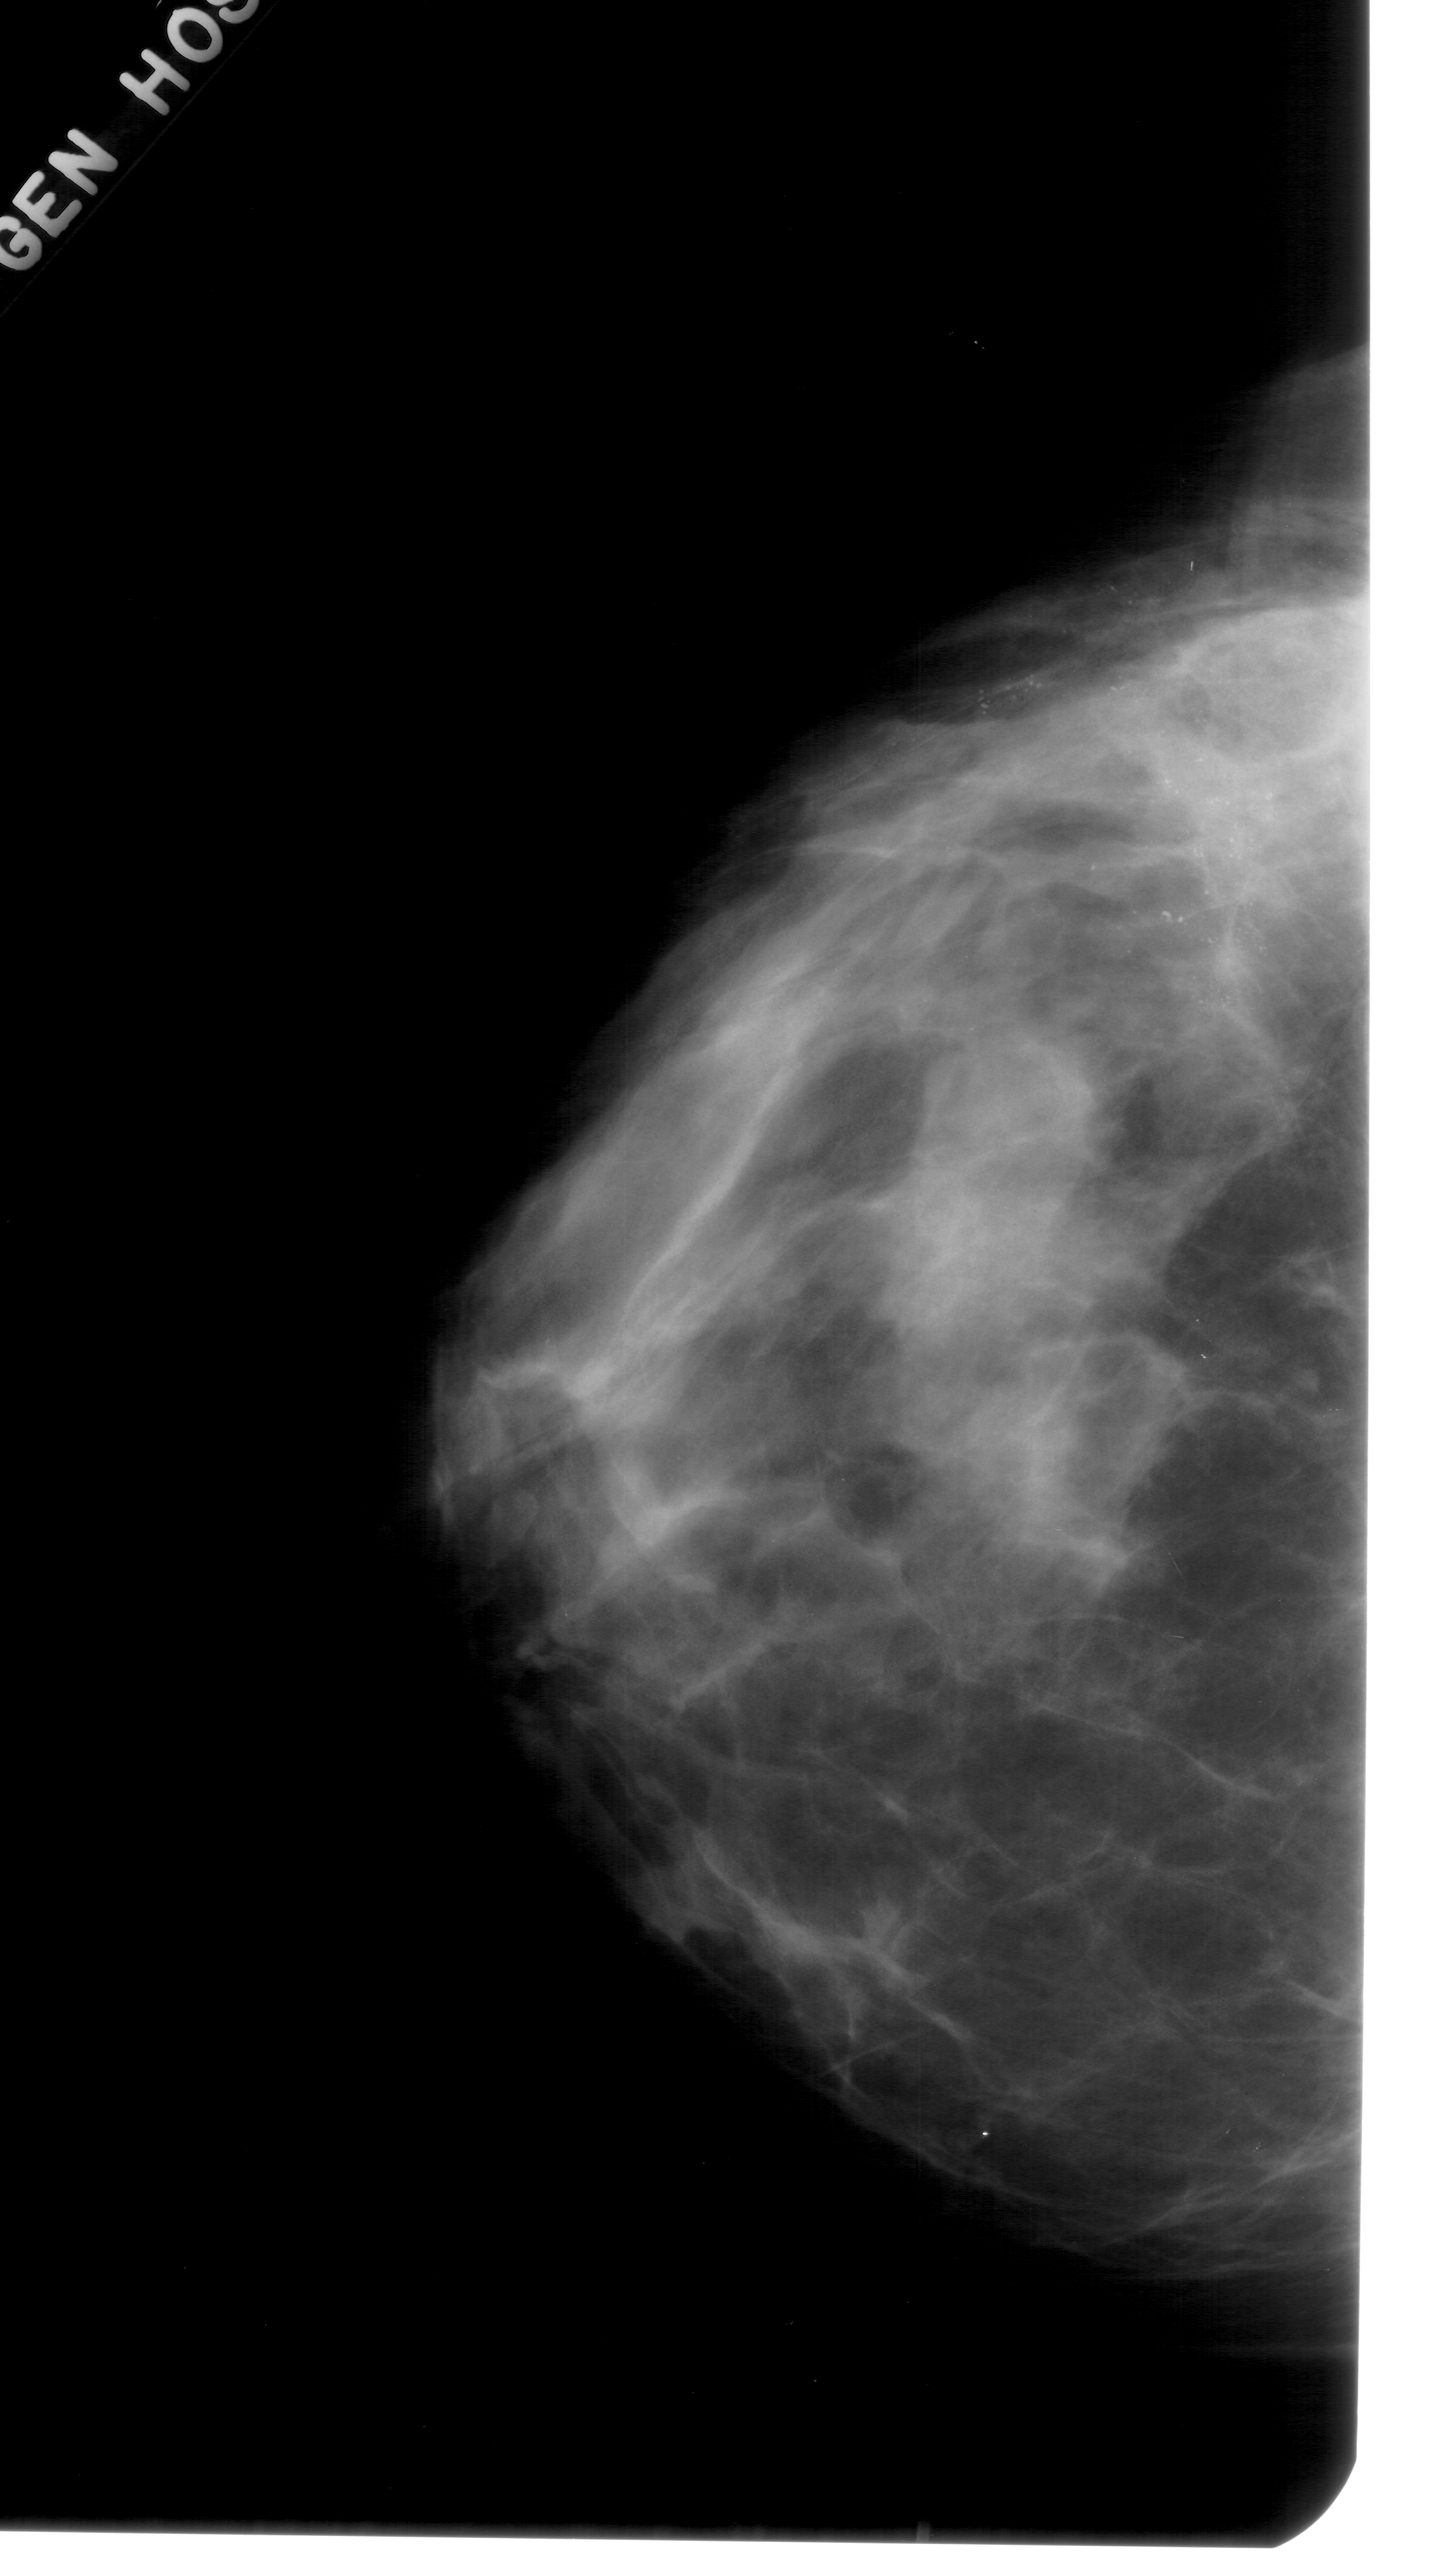
Digitized screen-film mammogram; left breast; CC view; BI-RADS breast density category 4 (scale 1–4); 1441 × 2576 image matrix.
Expert-marked regions of interest on this film, with their recorded descriptors:
- calcifications, morphology pleomorphic, distribution segmental; BI-RADS assessment category 5; subtlety rating 4 on a 1 (subtle) to 5 (obvious) scale; pathology result (as recorded, not read from the image): malignant: bounding box [x1, y1, x2, y2] px = [876, 534, 1366, 1054]